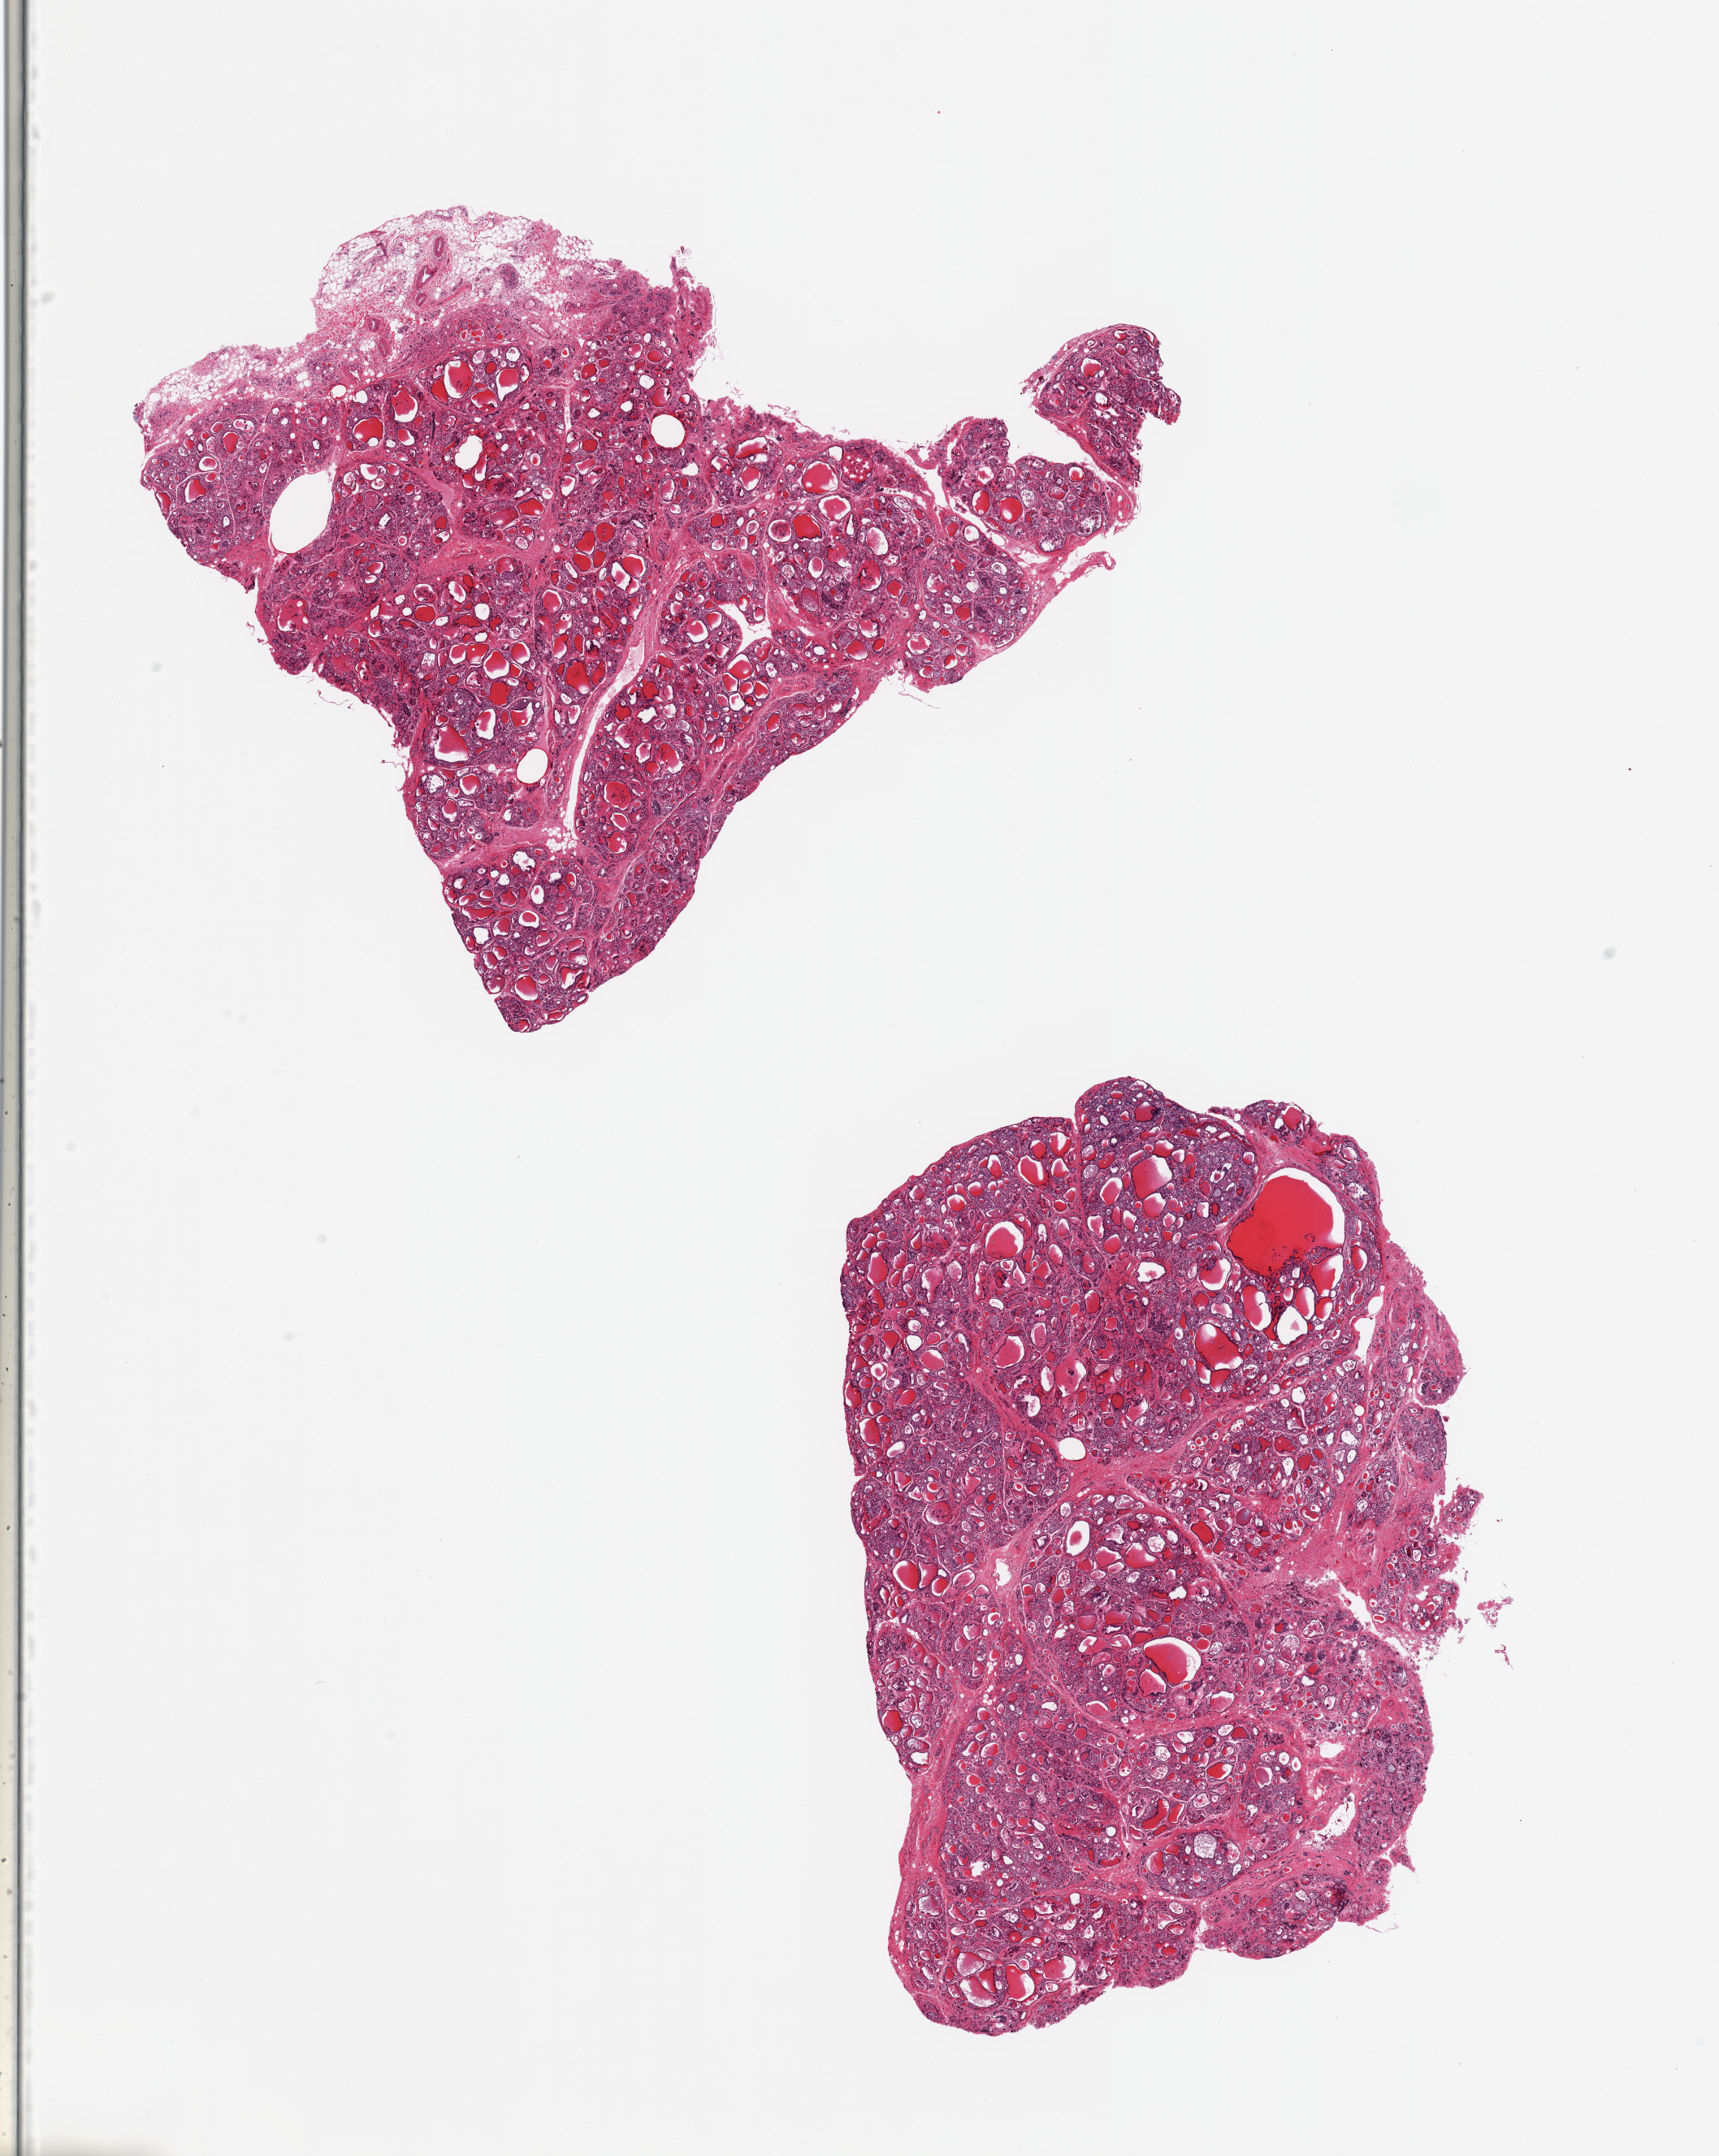
Whole-slide image, hematoxylin and eosin (H&E) stain — low-resolution overview of the scanned area, about 16.7 x 21.0 mm; PAXgene-fixed, paraffin-embedded tissue; sampled site (target tissue): thyroid; donor tissue sample. Male donor.
Review note (as recorded): 2 pieces, micronodular goitre; ~1mm colloid cyst noted.